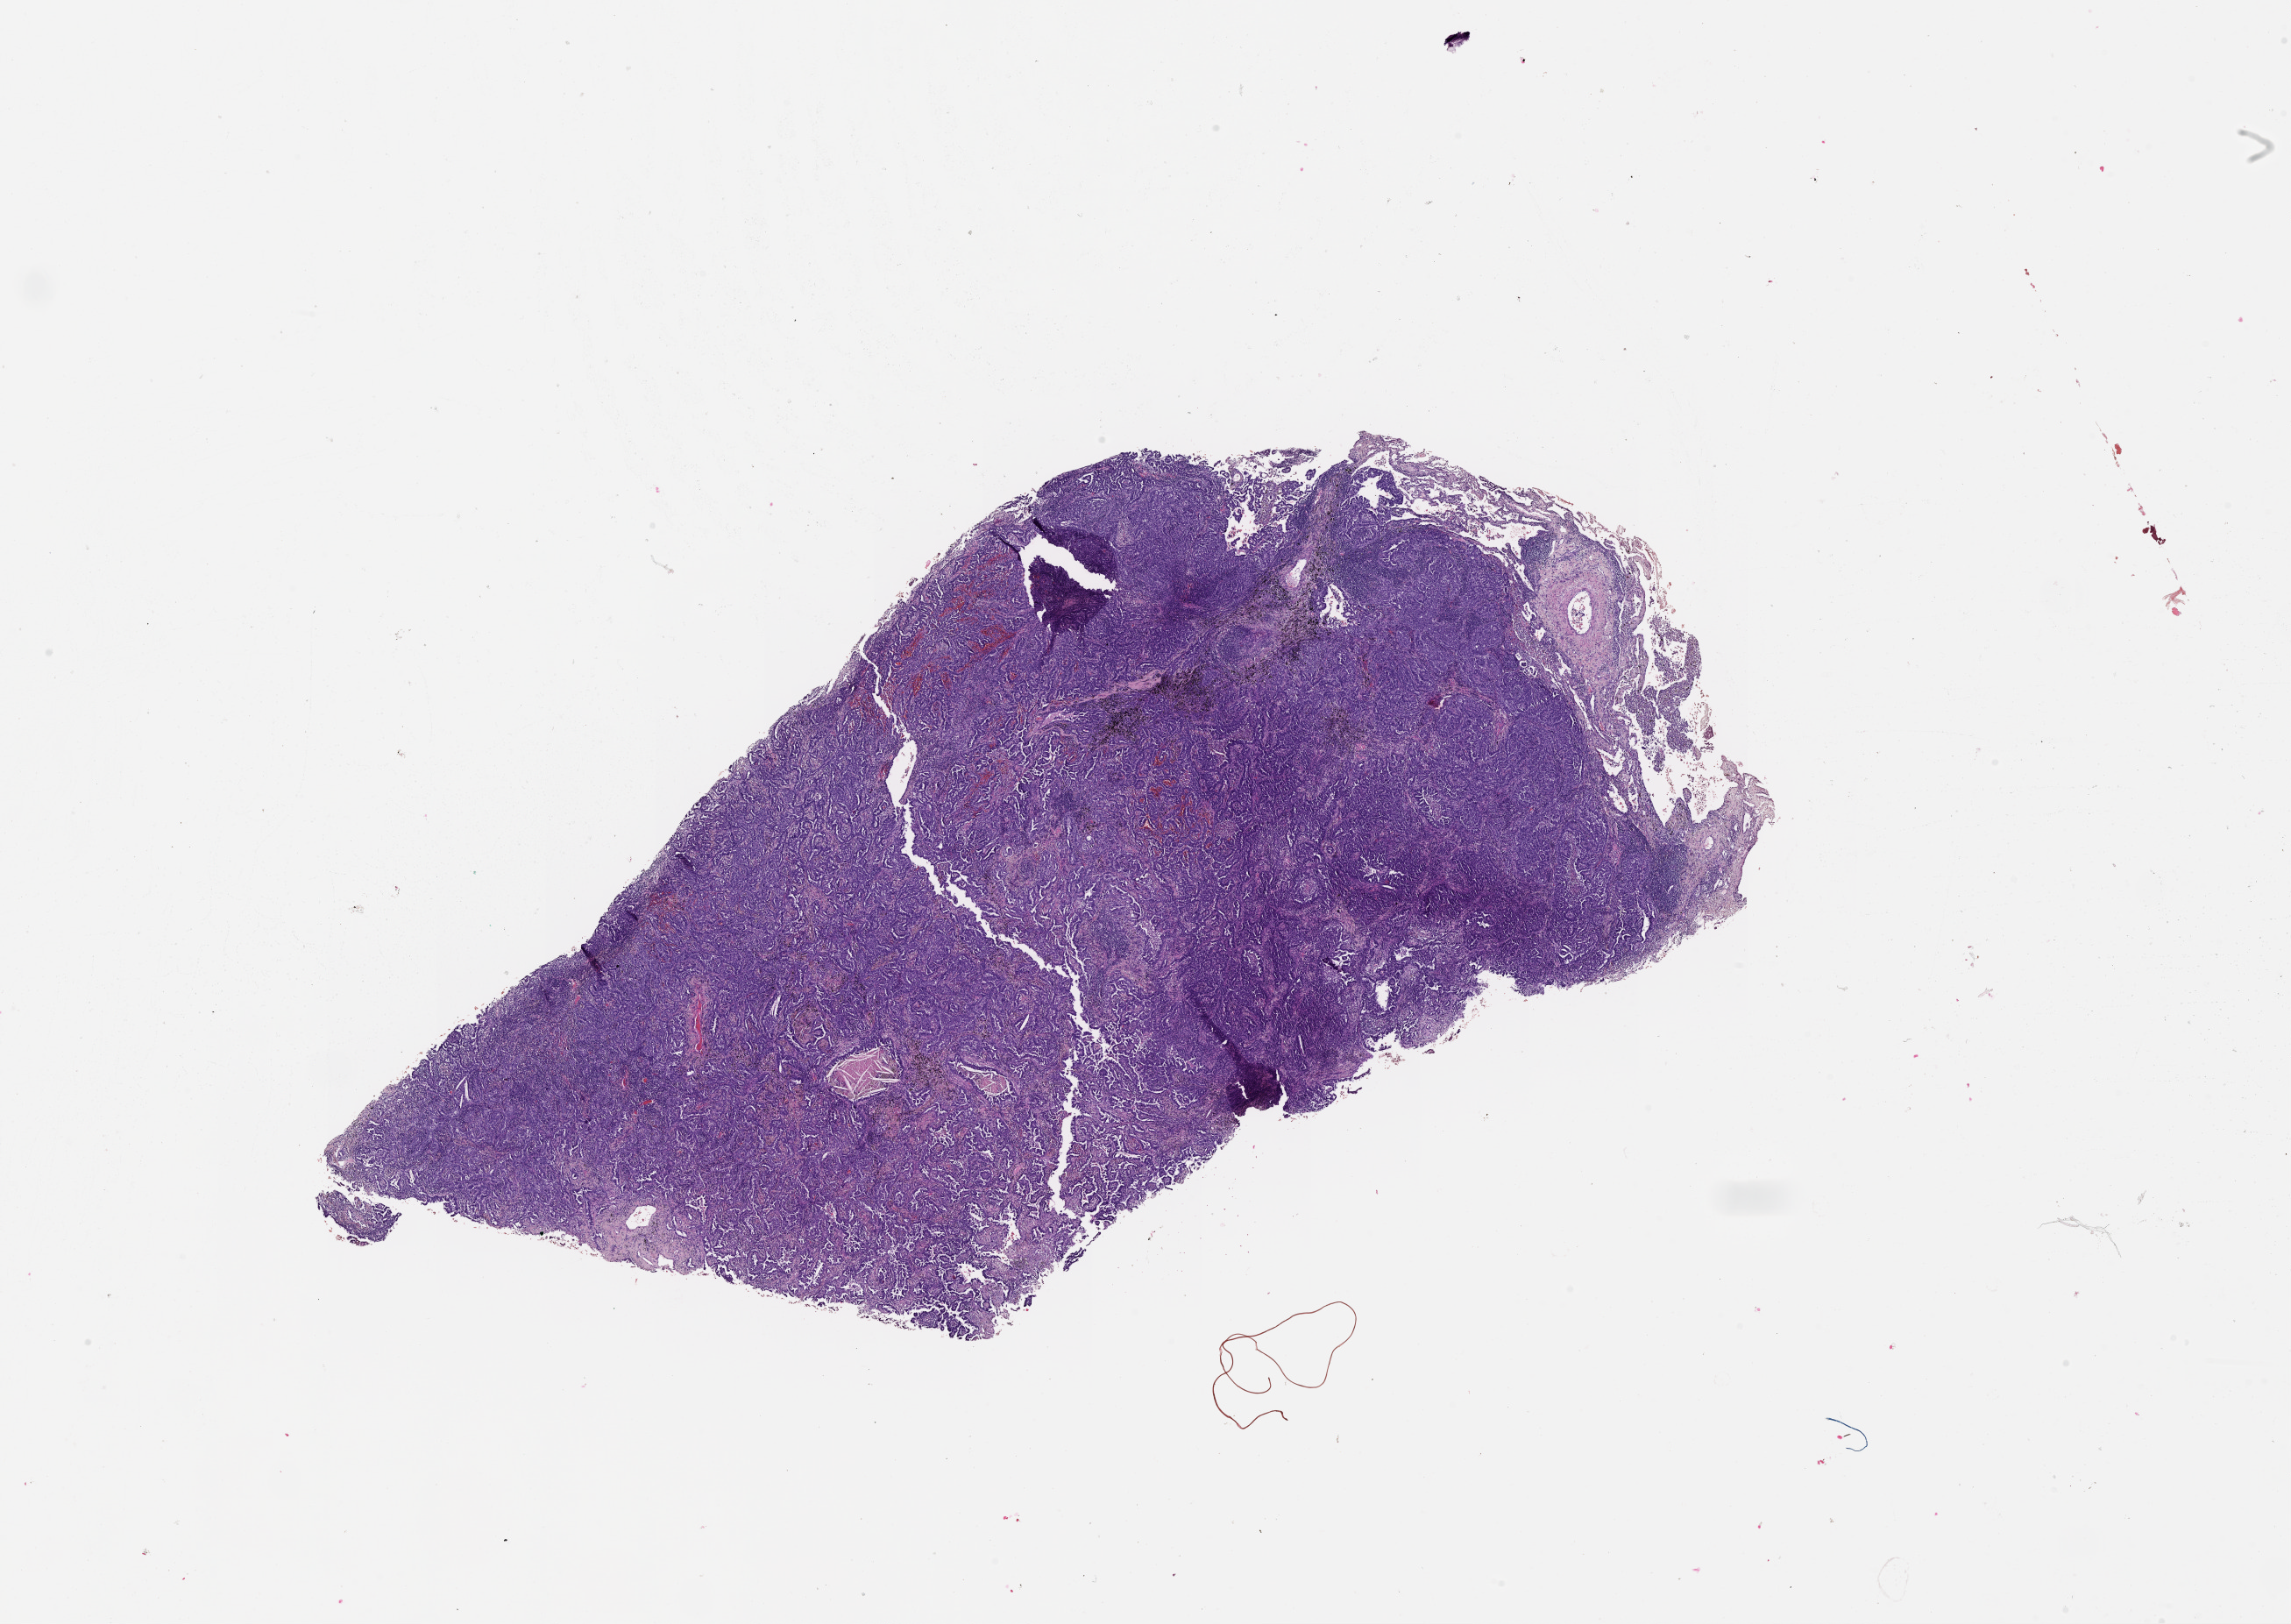
H&E-stained whole-slide image, a low-resolution overview of the entire scanned area, about 21.0 x 14.9 mm; tumour tissue sample, sampled site: lung. Male, 68 y/o. Histologic grade: G1 (well differentiated). Pathologist review of this section (percent, as recorded): tumour nuclei 80%, necrosis 3%.
Histologic diagnosis: Adenocarcinoma, NOS. AJCC pathologic stage: IB.